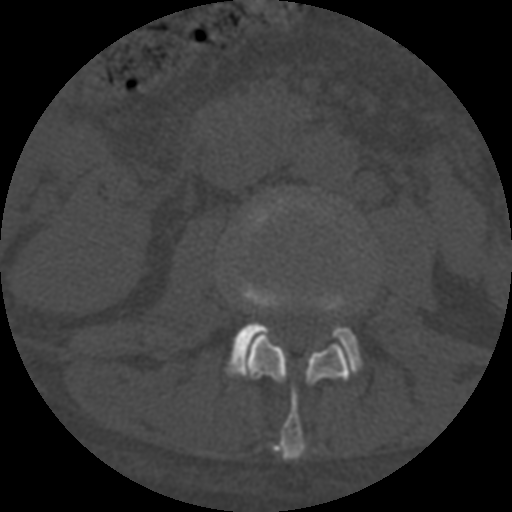
CT including the spine, one axial slice; position 247 of 708 along the scan axis; reconstruction kernel STANDARD; 120 kVp; one of 3 acquisitions stored at this slice position; bone window (W 1800 / L 400 HU); 512 × 512 image matrix, field of view 160 × 160 mm. Patient age 55 years. Case-level facts recorded for this patient, not image findings: primary cancer: colon.
Outlined on this slice (semi-automatically segmented with operator editing):
- L2 vertebra: box from (x=244, y=336) to (x=351, y=461) px
- L3 vertebra: (x=229, y=288)–(x=361, y=375)